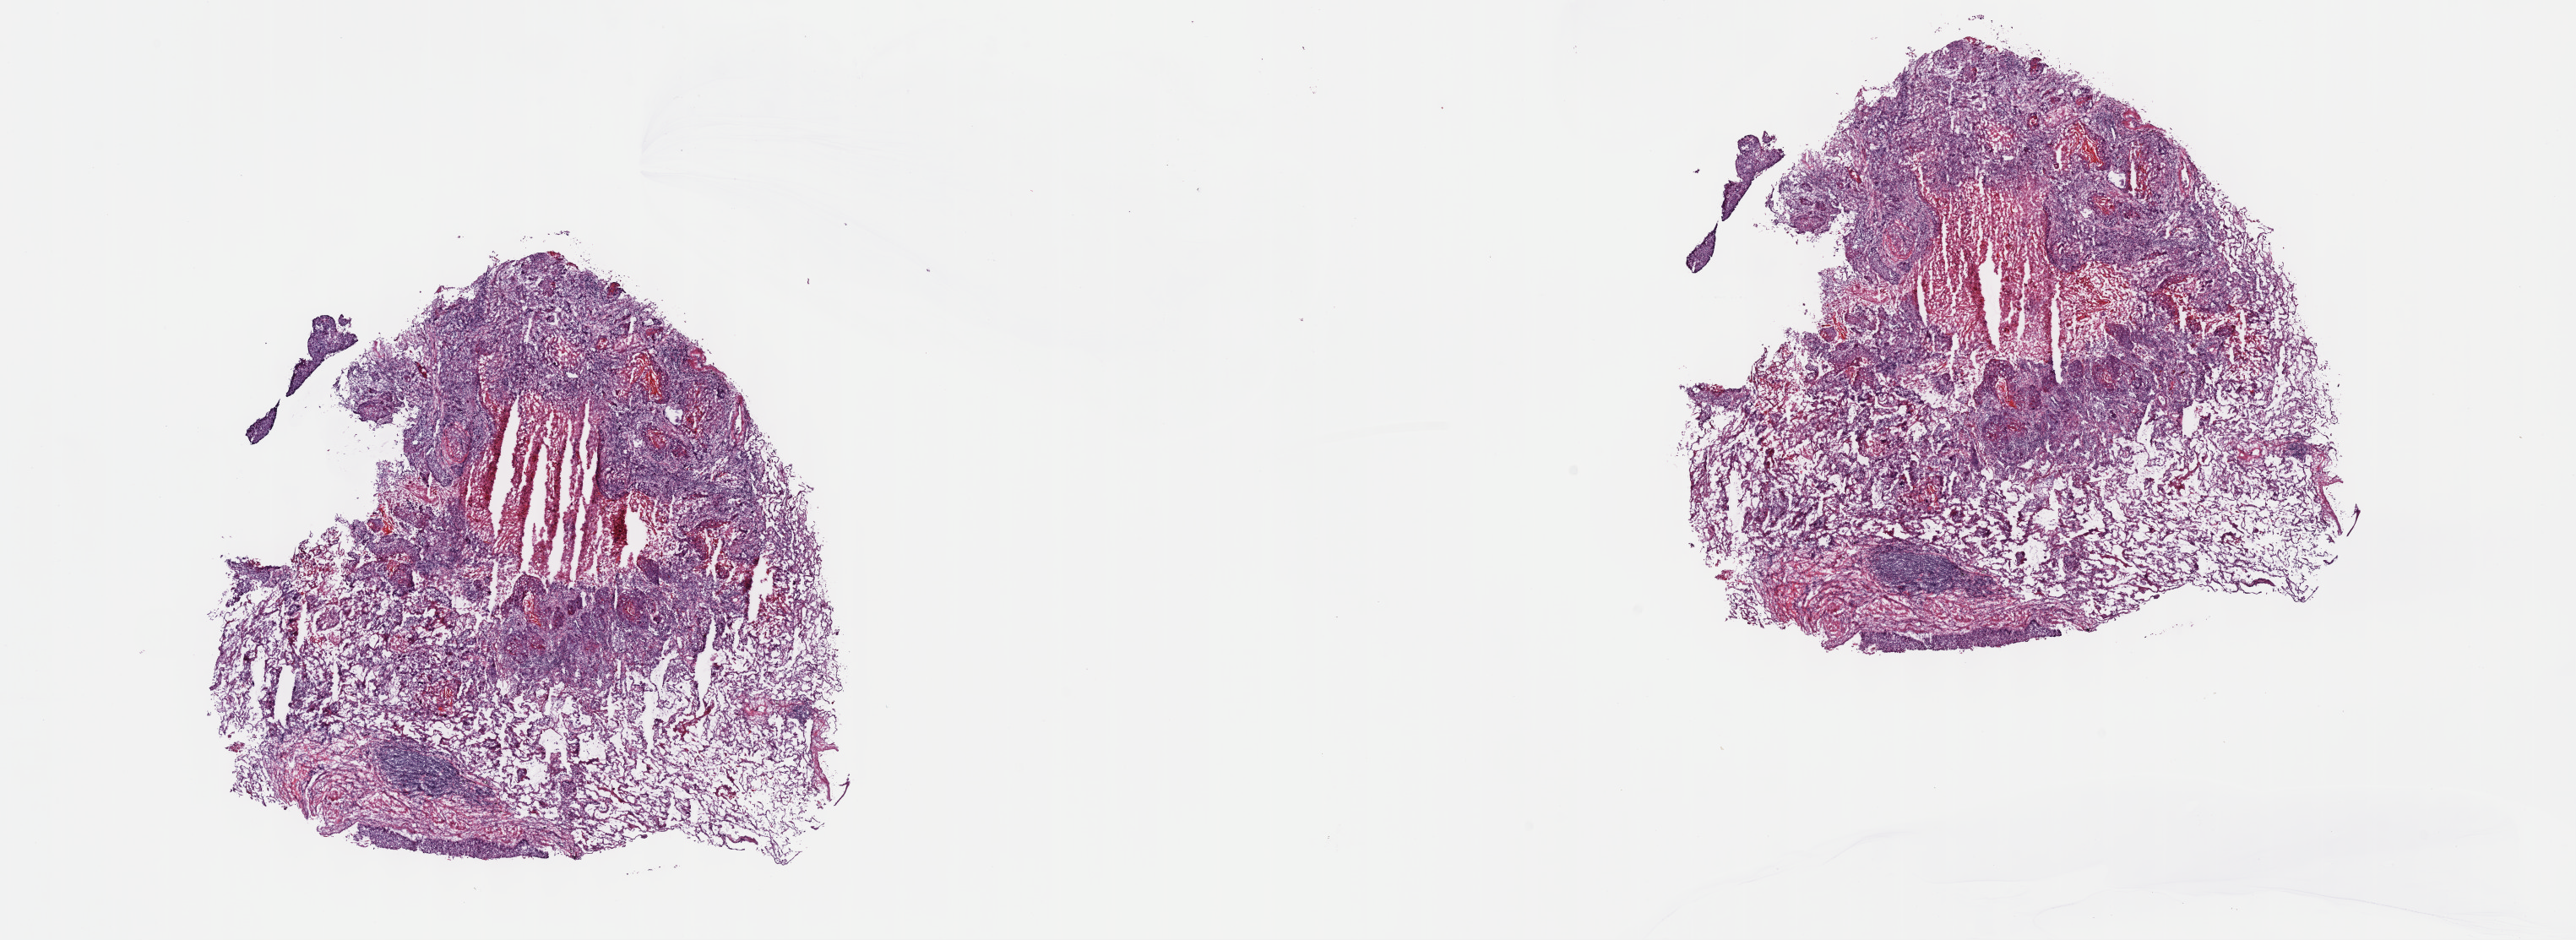
Digitized Hematoxylin and eosin (H&E) stained tissue section (whole slide), low-resolution overview of the scanned area, about 24.7 x 9.0 mm (slide scanned at 40x), frozen section, sample: primary tumour, lung. Female, age 77 years at initial diagnosis. Pathologist review of this section (percent, as recorded): tumour cells 83%, tumour nuclei 65%, normal cells 0%, stromal cells 0%, necrosis 17%. Inflammatory infiltration, as recorded: lymphocyte infiltration 5%, monocyte infiltration 0%, neutrophil infiltration 0%.
Diagnosis: Squamous cell carcinoma, NOS (lower lobe, lung). TNM: T1a N0 M0. AJCC pathologic stage: IA (7th edition).